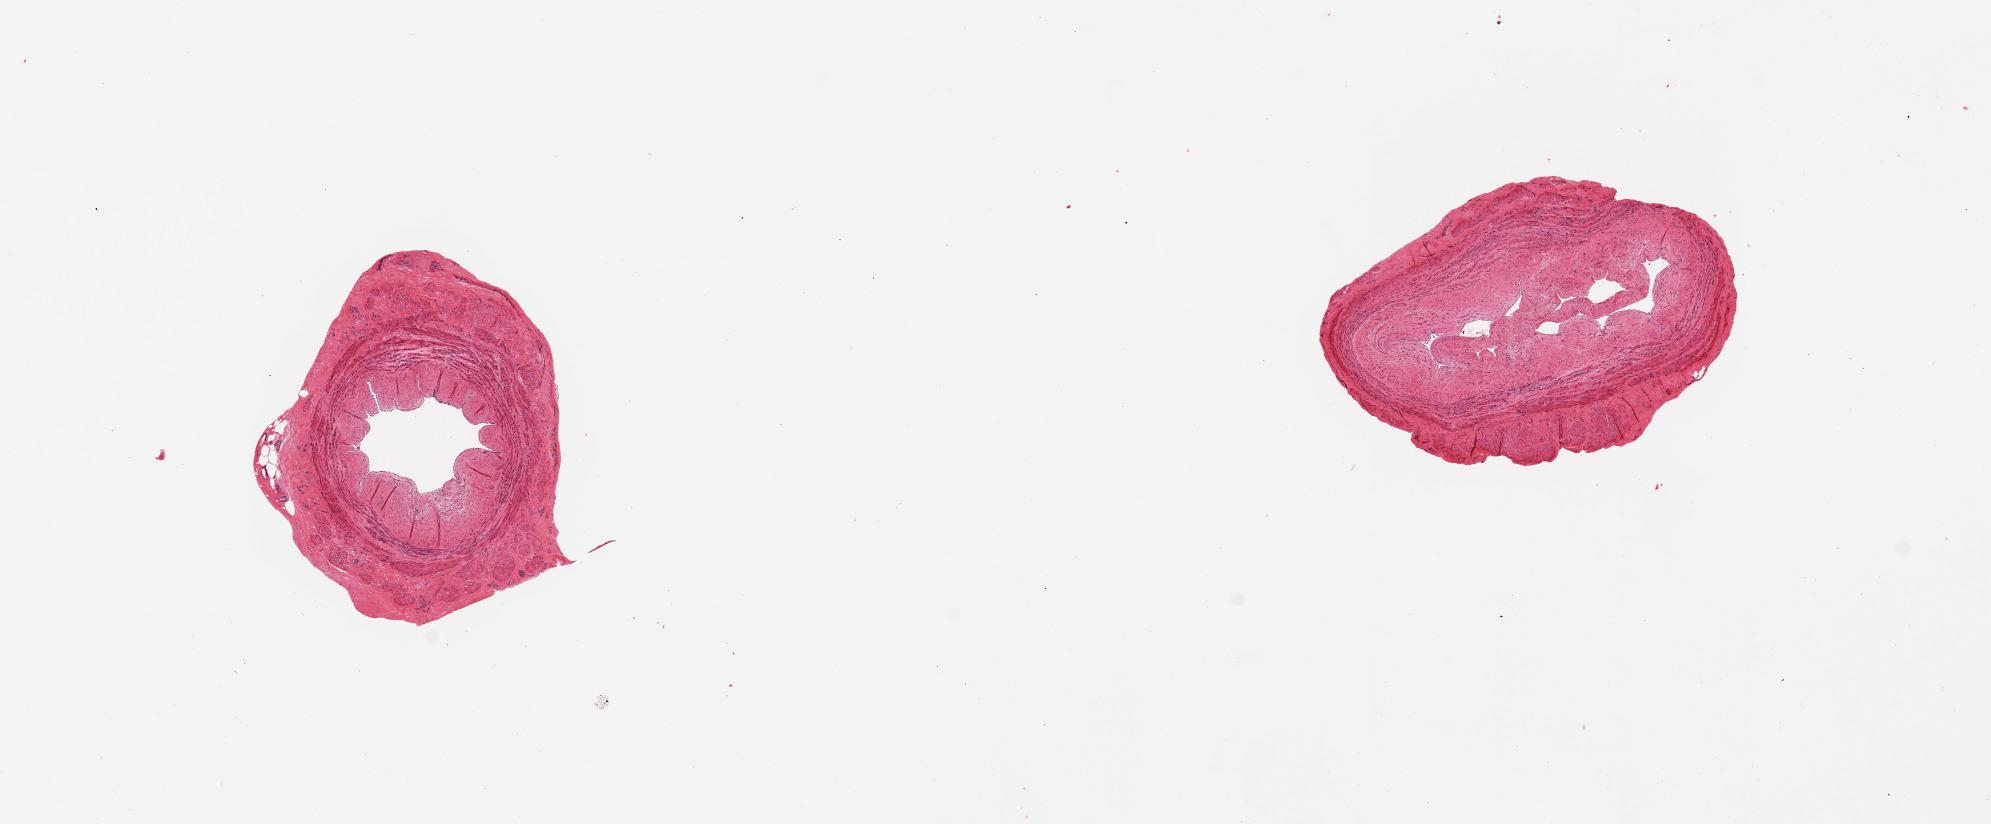
Whole-slide image, hematoxylin and eosin (H&E) stain, low-resolution overview of the scanned area, about 15.8 x 6.5 mm (slide scanned at 20x), PAXgene-fixed paraffin-embedded (PFPE) section, section of tibial artery (target tissue), tissue donor sample. Male donor.
- review note (as recorded): 2 pieces; well trimmed; intimal thickening